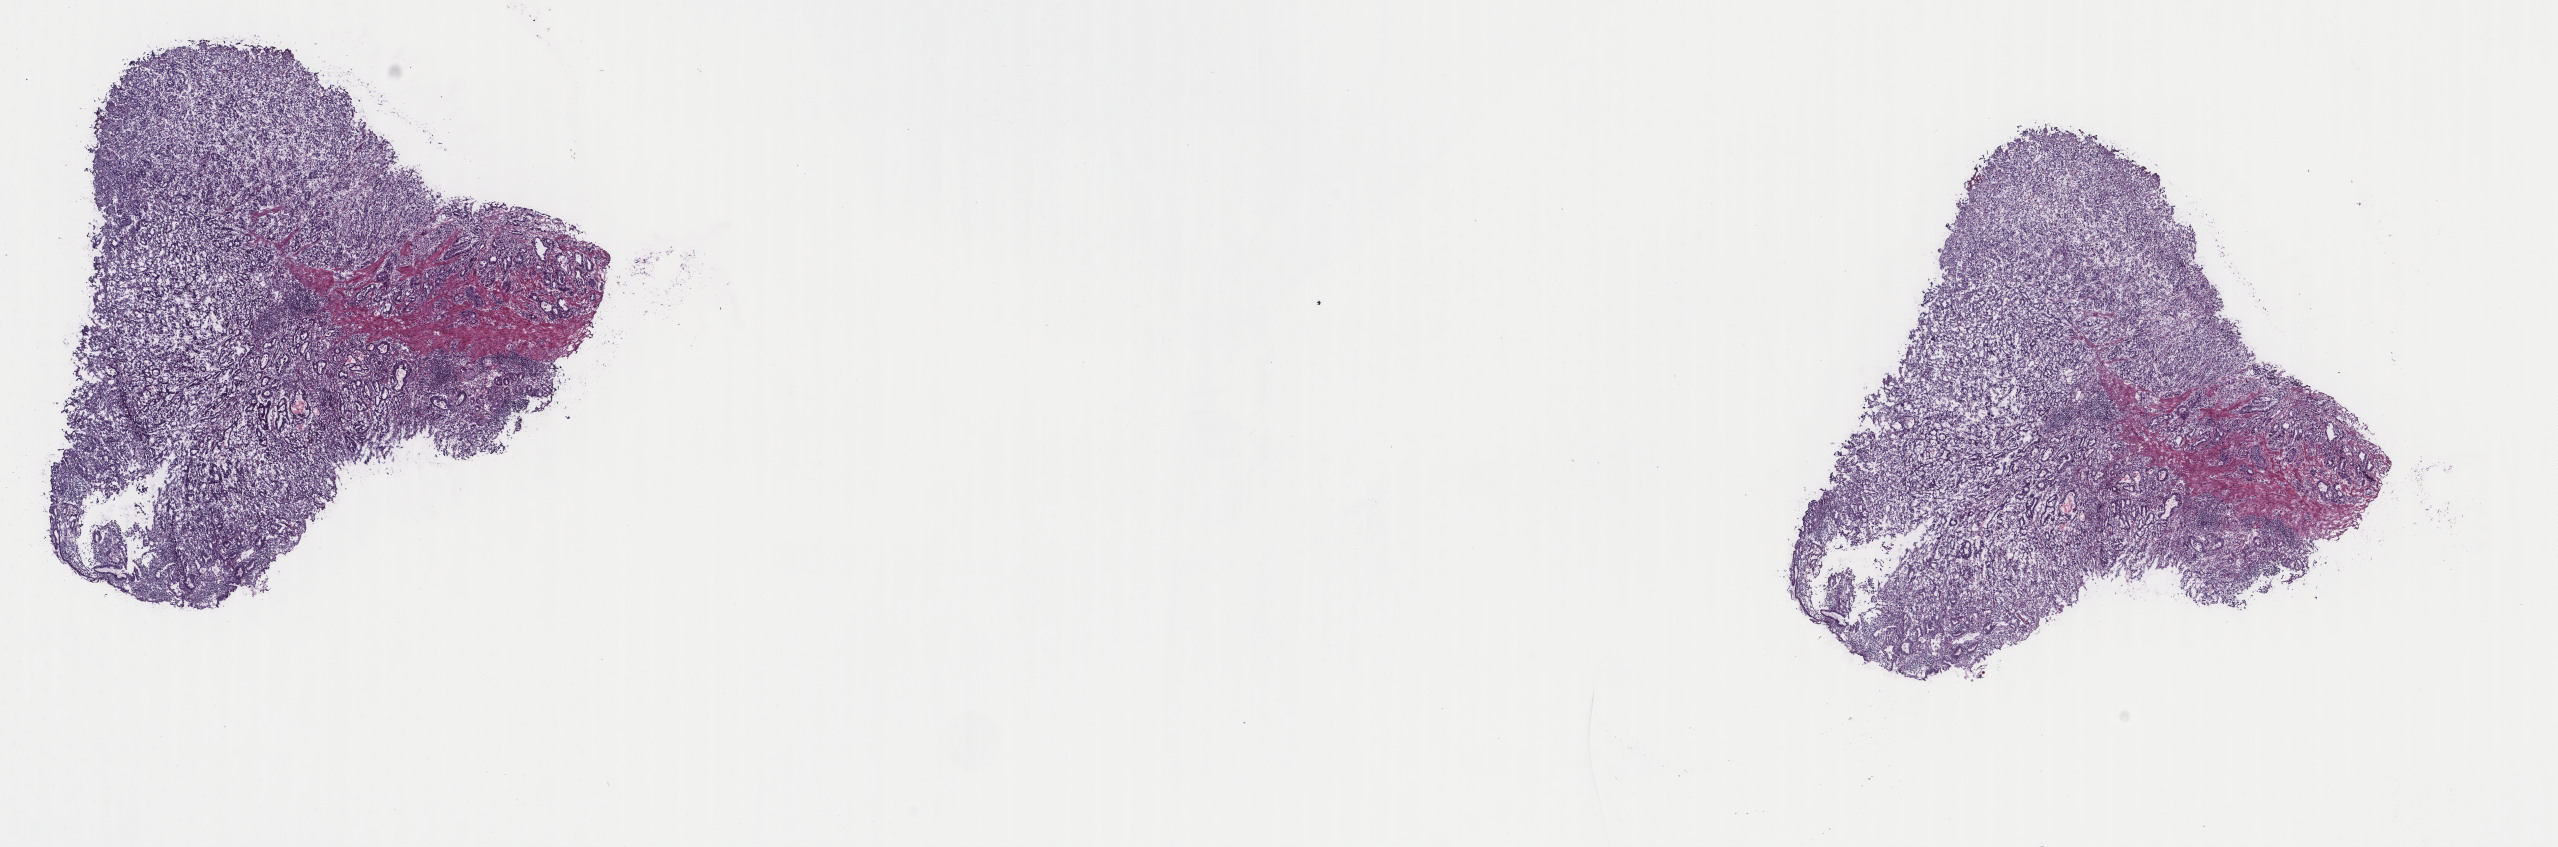
Digitized H&E tissue section (whole slide), a low-resolution overview of the entire scanned area, about 20.3 x 6.7 mm (from a 40x scan), frozen section from the top of the tissue portion, sample: primary tumour, stomach. Female, age 72 years at initial diagnosis. Histologic grade: G2 (moderately differentiated). Composition of this section per pathologist review: tumour cells 100%, tumour nuclei 80%, normal cells 0%, stromal cells 0%, necrosis 0%. Infiltration values recorded for this section: lymphocyte infiltration 3%, monocyte infiltration 0%, neutrophil infiltration 0%.
* pathologic diagnosis: Tubular adenocarcinoma (gastric antrum)
* AJCC pathologic stage: IIIA (7th edition)